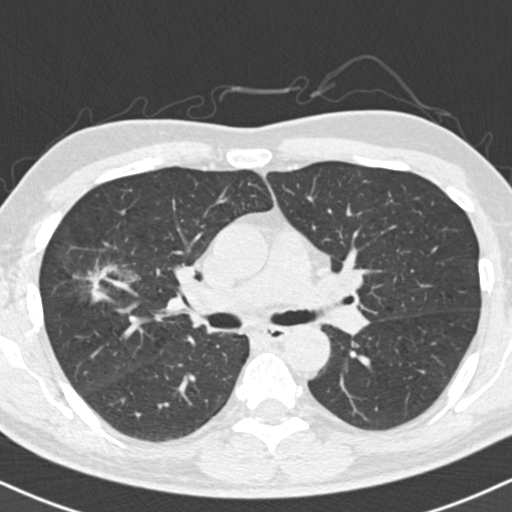
Axial slice from a low-dose chest CT screening exam. Baseline annual screen. Lung window (W 1500 / L -600 HU). 120 kVp. Slice 63 of 154 in the series. Male, age 56 years at enrolment. Former smoker at enrolment.
• Lesion marked by an expert reader, box from (x=56, y=253) to (x=146, y=318) px.
• Screening reader's record for this exam: no non-calcified nodule ≥4 mm recorded.
• Later outcome: lung cancer diagnosed 392 days after this screen (after the second annual screen) — bronchiolo-alveolar adenocarcinoma, NOS, right upper lobe, well differentiated (G1), stage IIB (AJCC 6th edition), 30 mm at pathology.